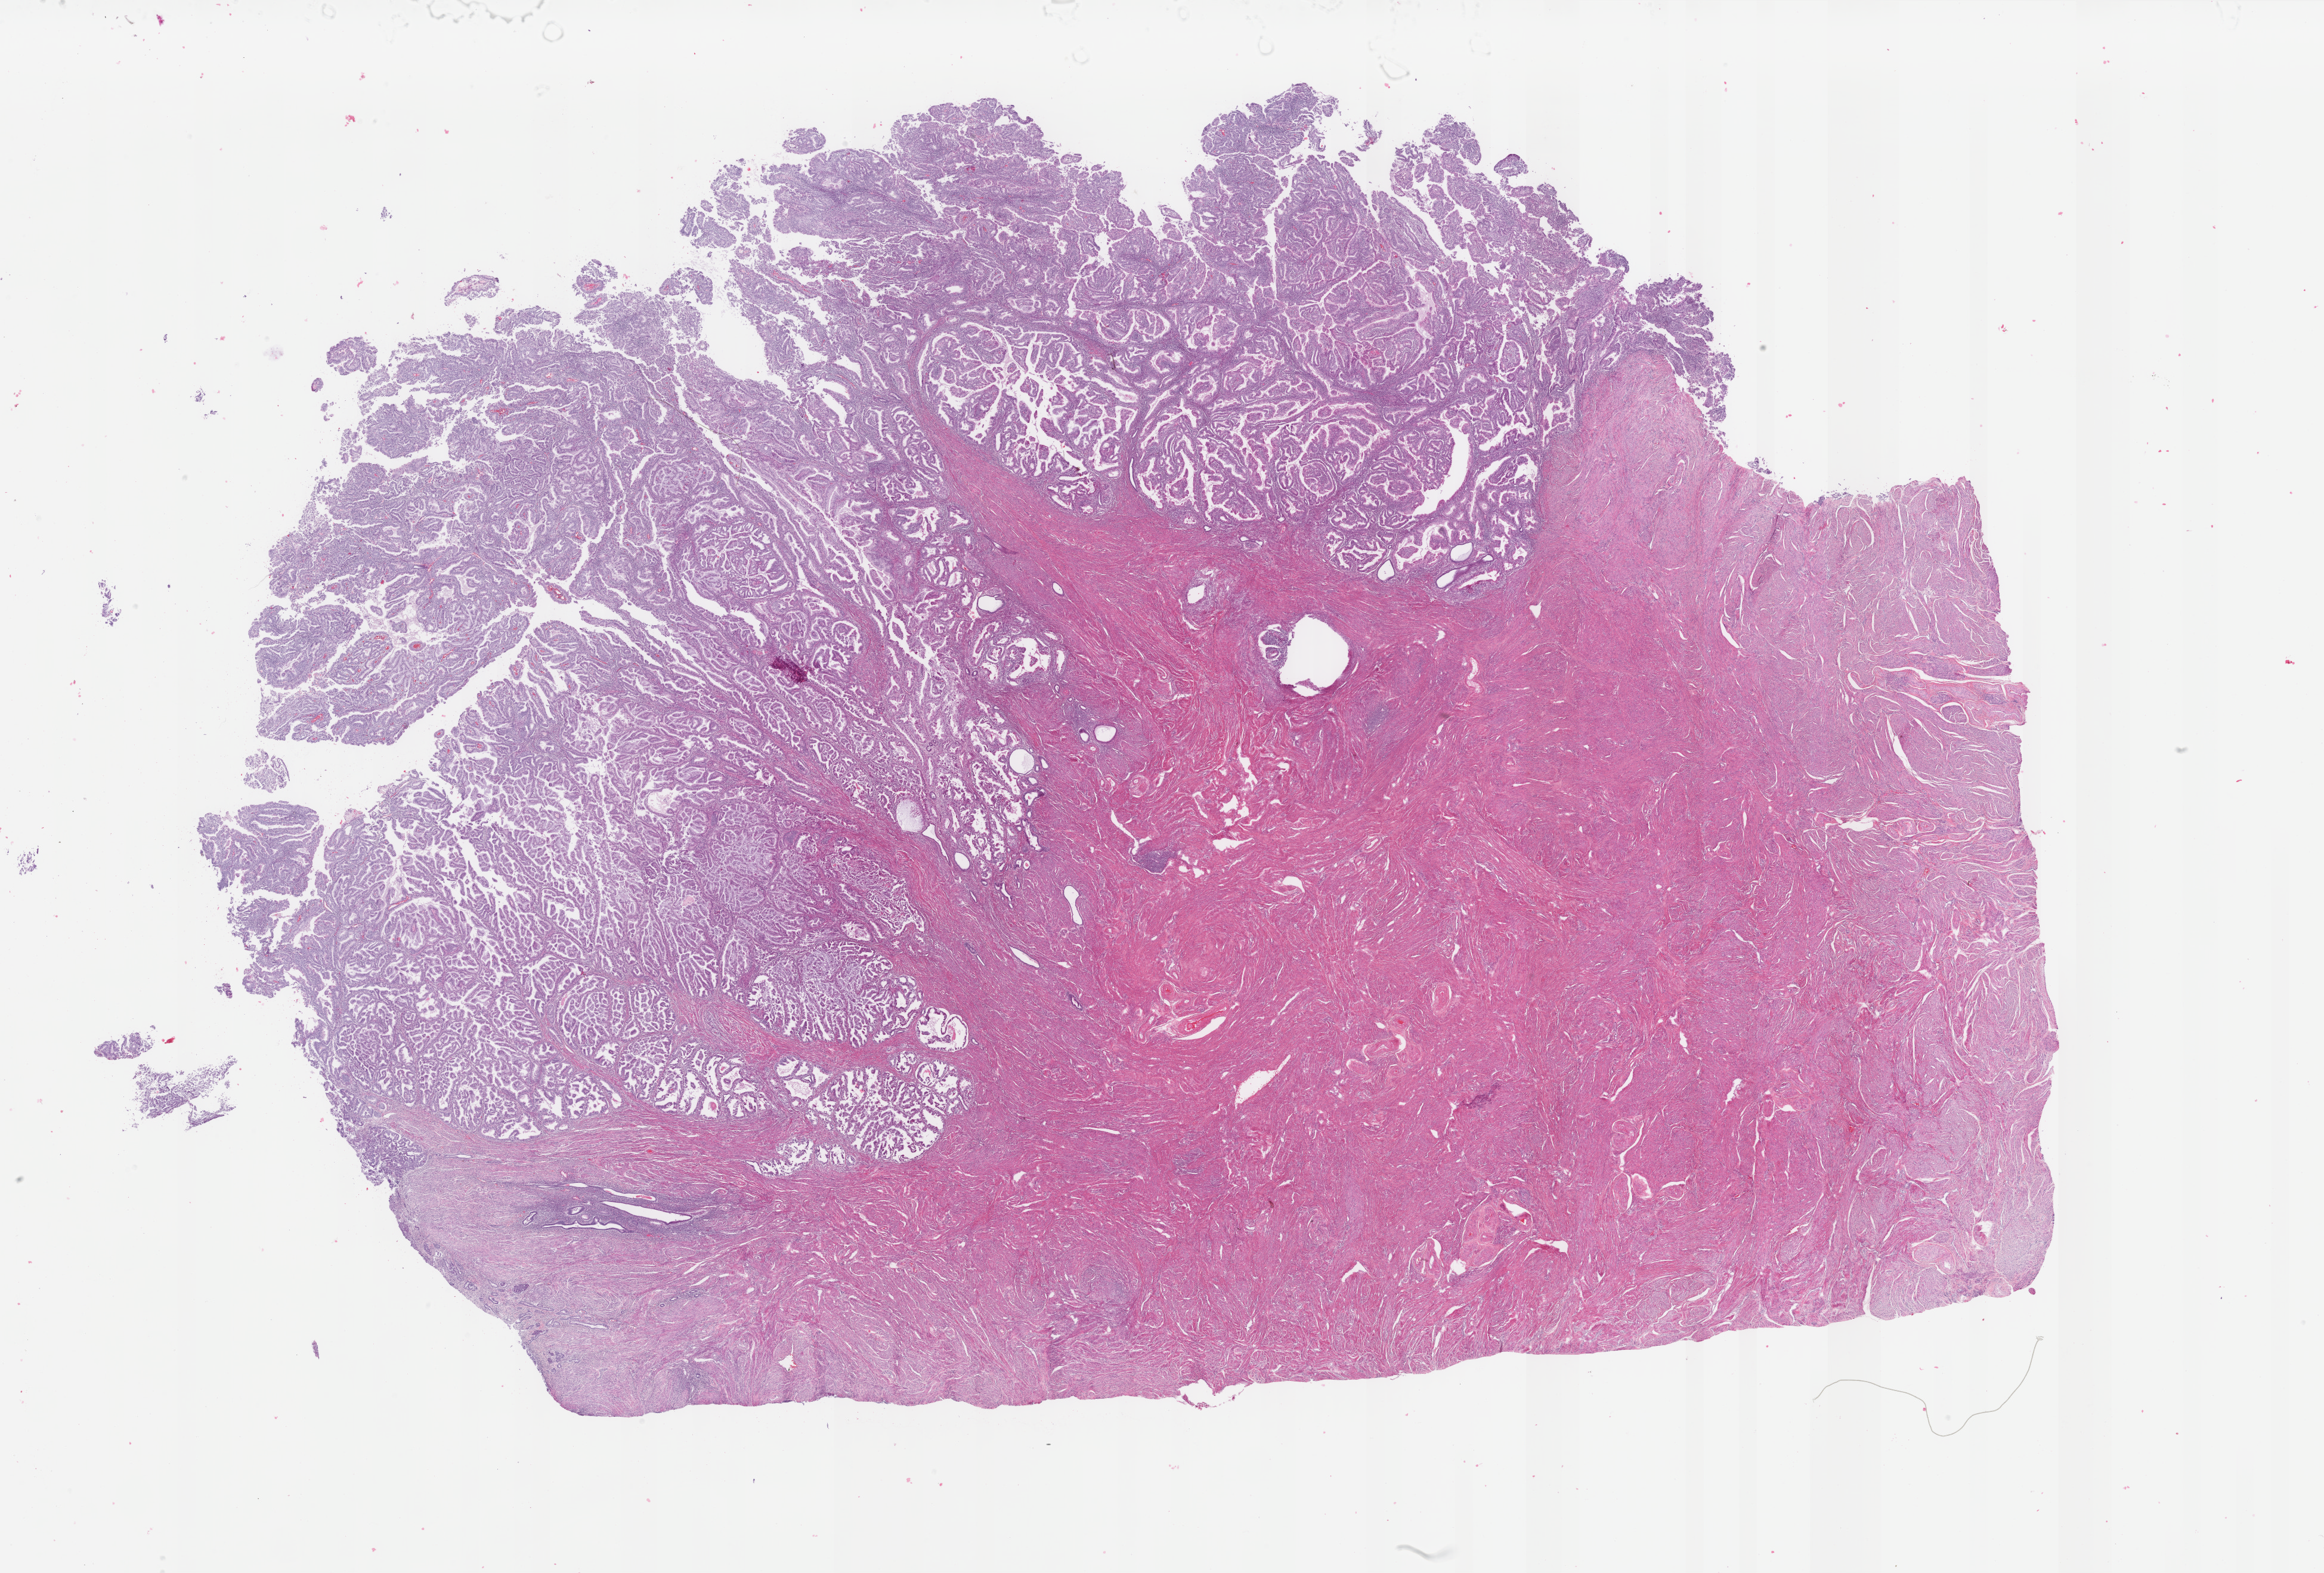
Whole-slide histology image, Hematoxylin and eosin (H&E) stained, low-resolution overview of the scanned area, about 30.9 x 20.9 mm. Formalin-fixed paraffin-embedded (FFPE) diagnostic section. Sample: primary tumour, uterus. Patient: female, age at initial diagnosis 54 years. Histologic grade: G1 (well differentiated).
Lymph nodes positive (case pathology): 0 of 28 examined. Pathologic diagnosis: Endometrioid adenocarcinoma, NOS (endometrium). FIGO stage: IA.